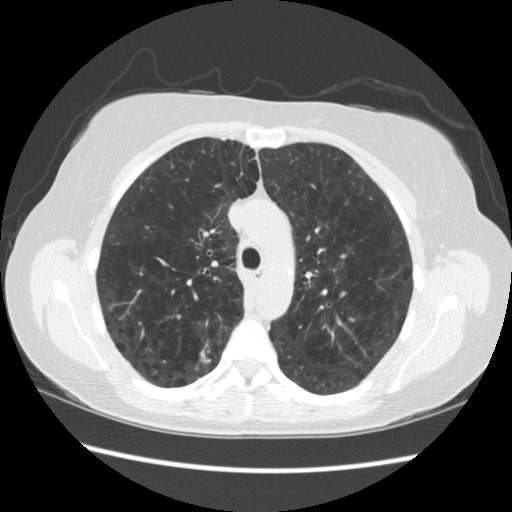
Axial slice from a low-dose chest CT screening exam. Third screening round (two years after baseline). Lung window (W 1500 / L -600 HU). Standard (soft-tissue) reconstruction kernel (STANDARD). Female, age 55 years at enrolment.
- Lesion marked by an expert reader, bounding box [x1, y1, x2, y2] px = [184, 336, 228, 374].
- Reader record for this screening exam (exam-level; its link to the box is not recorded): non-calcified nodule or mass ≥4 mm, right upper lobe, 11 × 11 mm, poorly defined margins, soft tissue attenuation, pre-existing on the prior screen: no.
- Later outcome: lung cancer diagnosed 96 days after this screen — small cell carcinoma, NOS, right upper lobe.